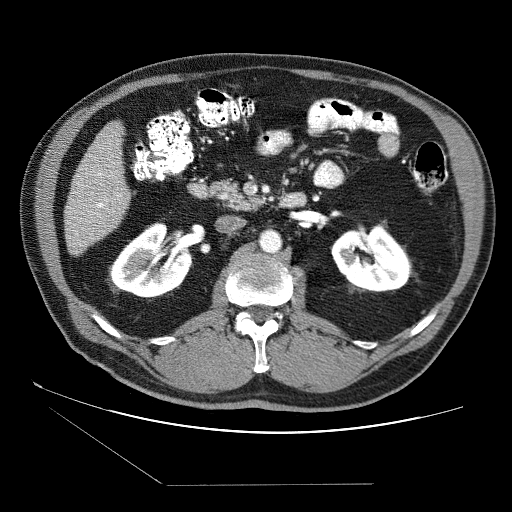
Contrast-enhanced abdominal CT (liver protocol), one axial slice. Slice 17 of 87 in the series (ordered by position). 120 kVp. Soft-tissue window (W 400 / L 40 HU). 2.5 mm slice thickness. 512 × 512 image matrix, field of view 400 × 400 mm. Case-level facts recorded for this patient, not image findings: diagnosis: hepatocellular carcinoma (patient treated with transarterial chemoembolisation; whether this scan precedes or follows treatment is not stated here); TNM stage (as recorded): Stage-II; Child-Pugh class: B; tumour differentiation: no biopsy; tumour size: 2.6 cm.
Annotated regions visible in this slice (semi-automatic segmentation, software-assisted and operator-edited):
- liver parenchyma outside the tumour (the mass and vessels are separate outlines, so this box may not span the whole liver): bounding box <64,122,130,256> (left, top, right, bottom; pixels)
- liver vessels: <70,141,121,235>